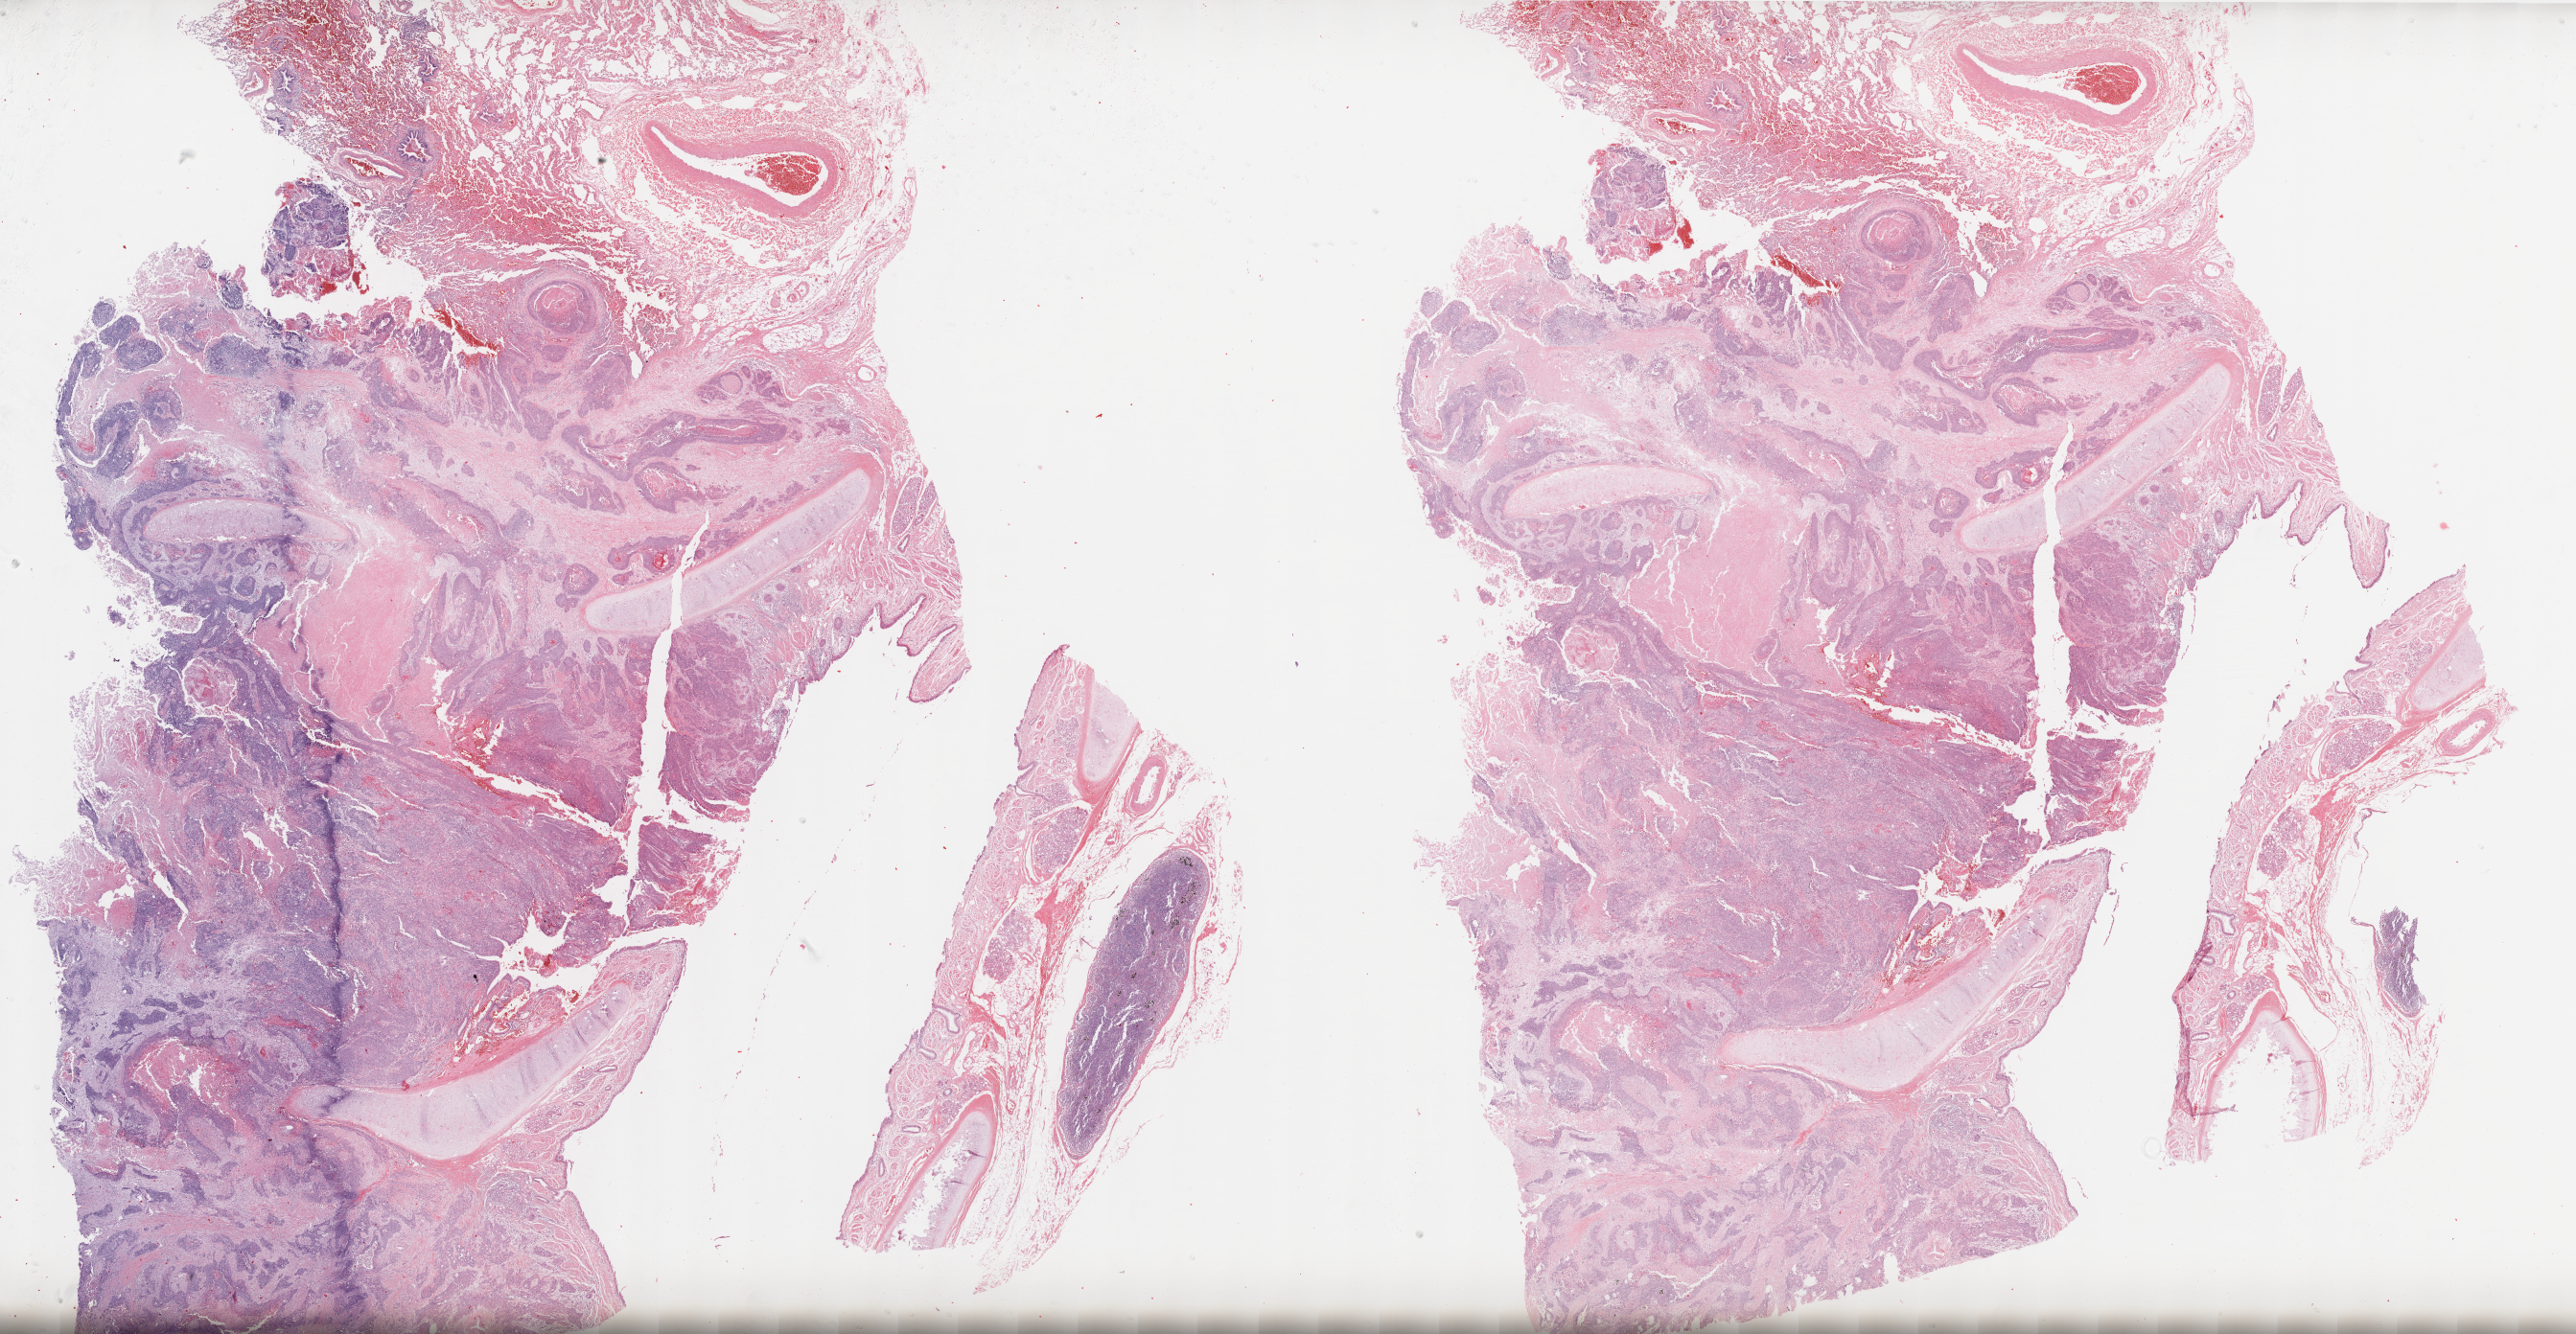
Digitized H&E-stained tissue section (whole slide), low-resolution overview of the scanned area, about 43.2 x 22.4 mm (from a 20x scan), FFPE section, lung, primary tumour sample. Male, age 62 years at initial diagnosis.
Diagnosis: Squamous cell carcinoma, NOS. TNM: T2 N1 M0. AJCC pathologic stage: IIB.